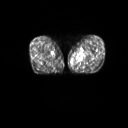
FDG PET of an extremity soft-tissue mass (from a PET/CT study), one axial slice; slice 11 of 267 in the series (ordered by position); 3.27 mm slice thickness; 128 × 128 image matrix, field of view 600 × 600 mm. Male patient, age 59 years. From the clinical record (not read from this slice): histological type: pleiomorphic liposarcoma; grade: high; site of the primary tumour: left thigh.
Outlined on this slice (expert contour drawn on MRI and transferred to this co-registered scan by the dataset authors):
- gross tumour volume including surrounding oedema: bounding box <77,52,88,63> (left, top, right, bottom; pixels)